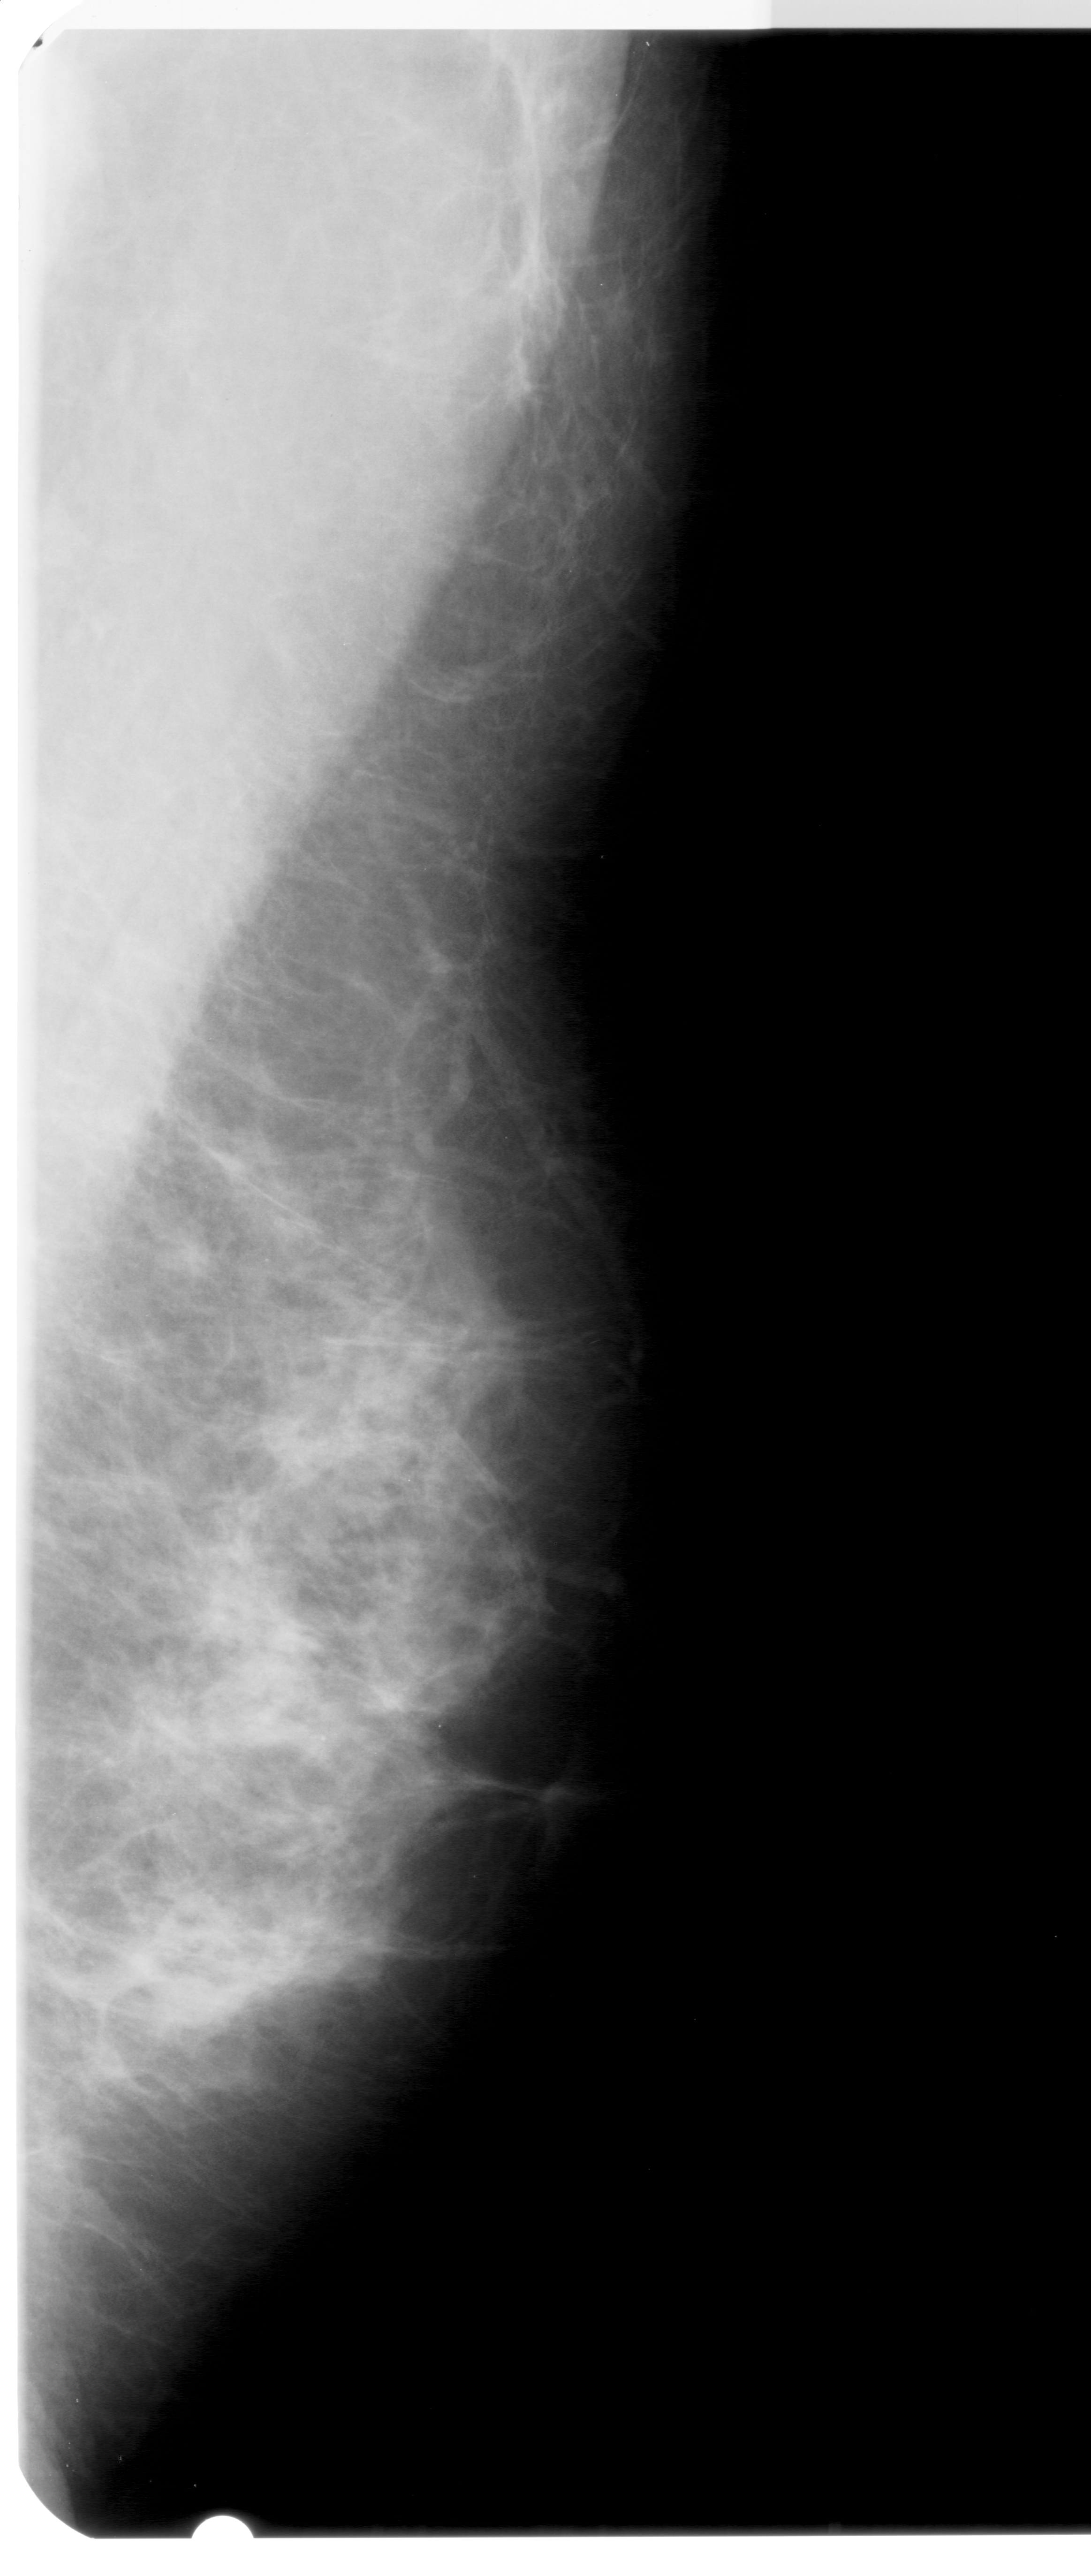
Mammogram (digitized film); right breast; mediolateral oblique (MLO) view; BI-RADS breast density category 4 (scale 1–4).
Mass, shape architectural distortion, margins ill defined; BI-RADS assessment category 4; pathology result (as recorded, not read from the image): benign.